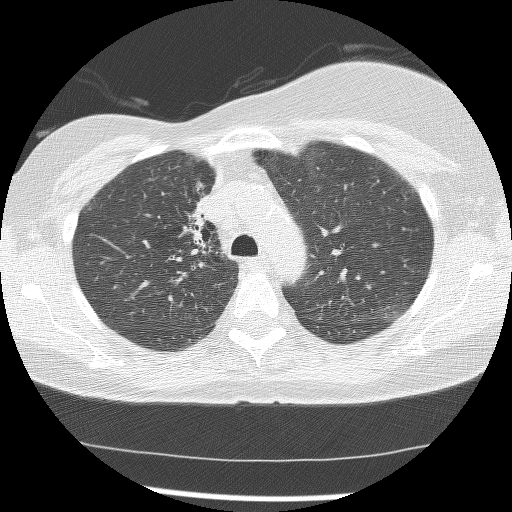
Low-dose screening chest CT, axial slice; first (baseline) screen; lung window (W 1500 / L -600 HU); 2.5 mm slice thickness; lung (sharp) reconstruction kernel (BONE); slice 42 of 172 in the series. Female participant, aged 56 years at enrolment. Current smoker at enrolment.
Expert-annotated lung lesion, bounding box [x1, y1, x2, y2] px = [164, 187, 222, 271]. The screening reader recorded 2 non-calcified nodules or masses ≥4 mm on this exam (right lower lobe, right middle lobe); which of them this box marks is not recorded. Lung cancer was diagnosed 1185 days after this screen: adenocarcinoma, NOS, right upper lobe, stage IIIB (AJCC 6th edition), 8 mm at pathology.